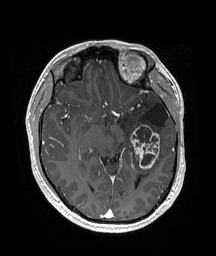
Brain MRI from a brain-tumour surgery series, one axial slice. Slice 101 of 192 in the series (ordered by position). T1-weighted post-contrast. 1 mm slice thickness. 216 × 256 image matrix. From the clinical record (not read from this slice): histopathology: Glioneuronal tumor; WHO grade: 2.
Outlined on this slice (outlined manually by an expert reader):
- previous resection cavity: bounding box <145,104,168,127> (left, top, right, bottom; pixels)
- tumour: <130,124,160,169>